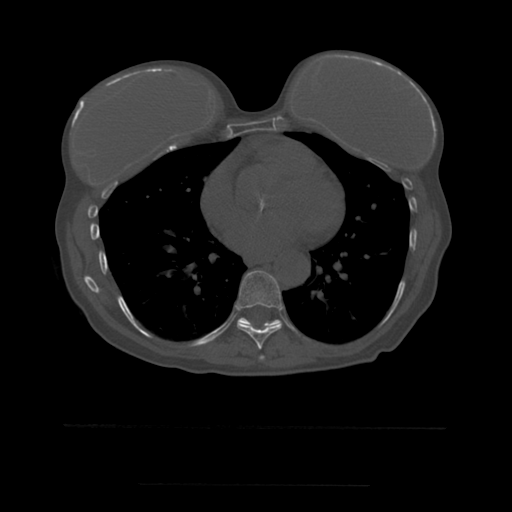
CT including the spine, one axial slice; bone window (W 1800 / L 400 HU); 512 × 512 image matrix, field of view 350 × 350 mm. Patient age 58 years. From the clinical record (not read from this slice): primary cancer: lung.
Structures marked on this image (semi-automatically segmented with operator editing):
- T7 vertebra: box from (x=260, y=356) to (x=265, y=360) px
- T8 vertebra: (x=237, y=271)–(x=283, y=350)
- T9 vertebra: (x=238, y=318)–(x=280, y=327)